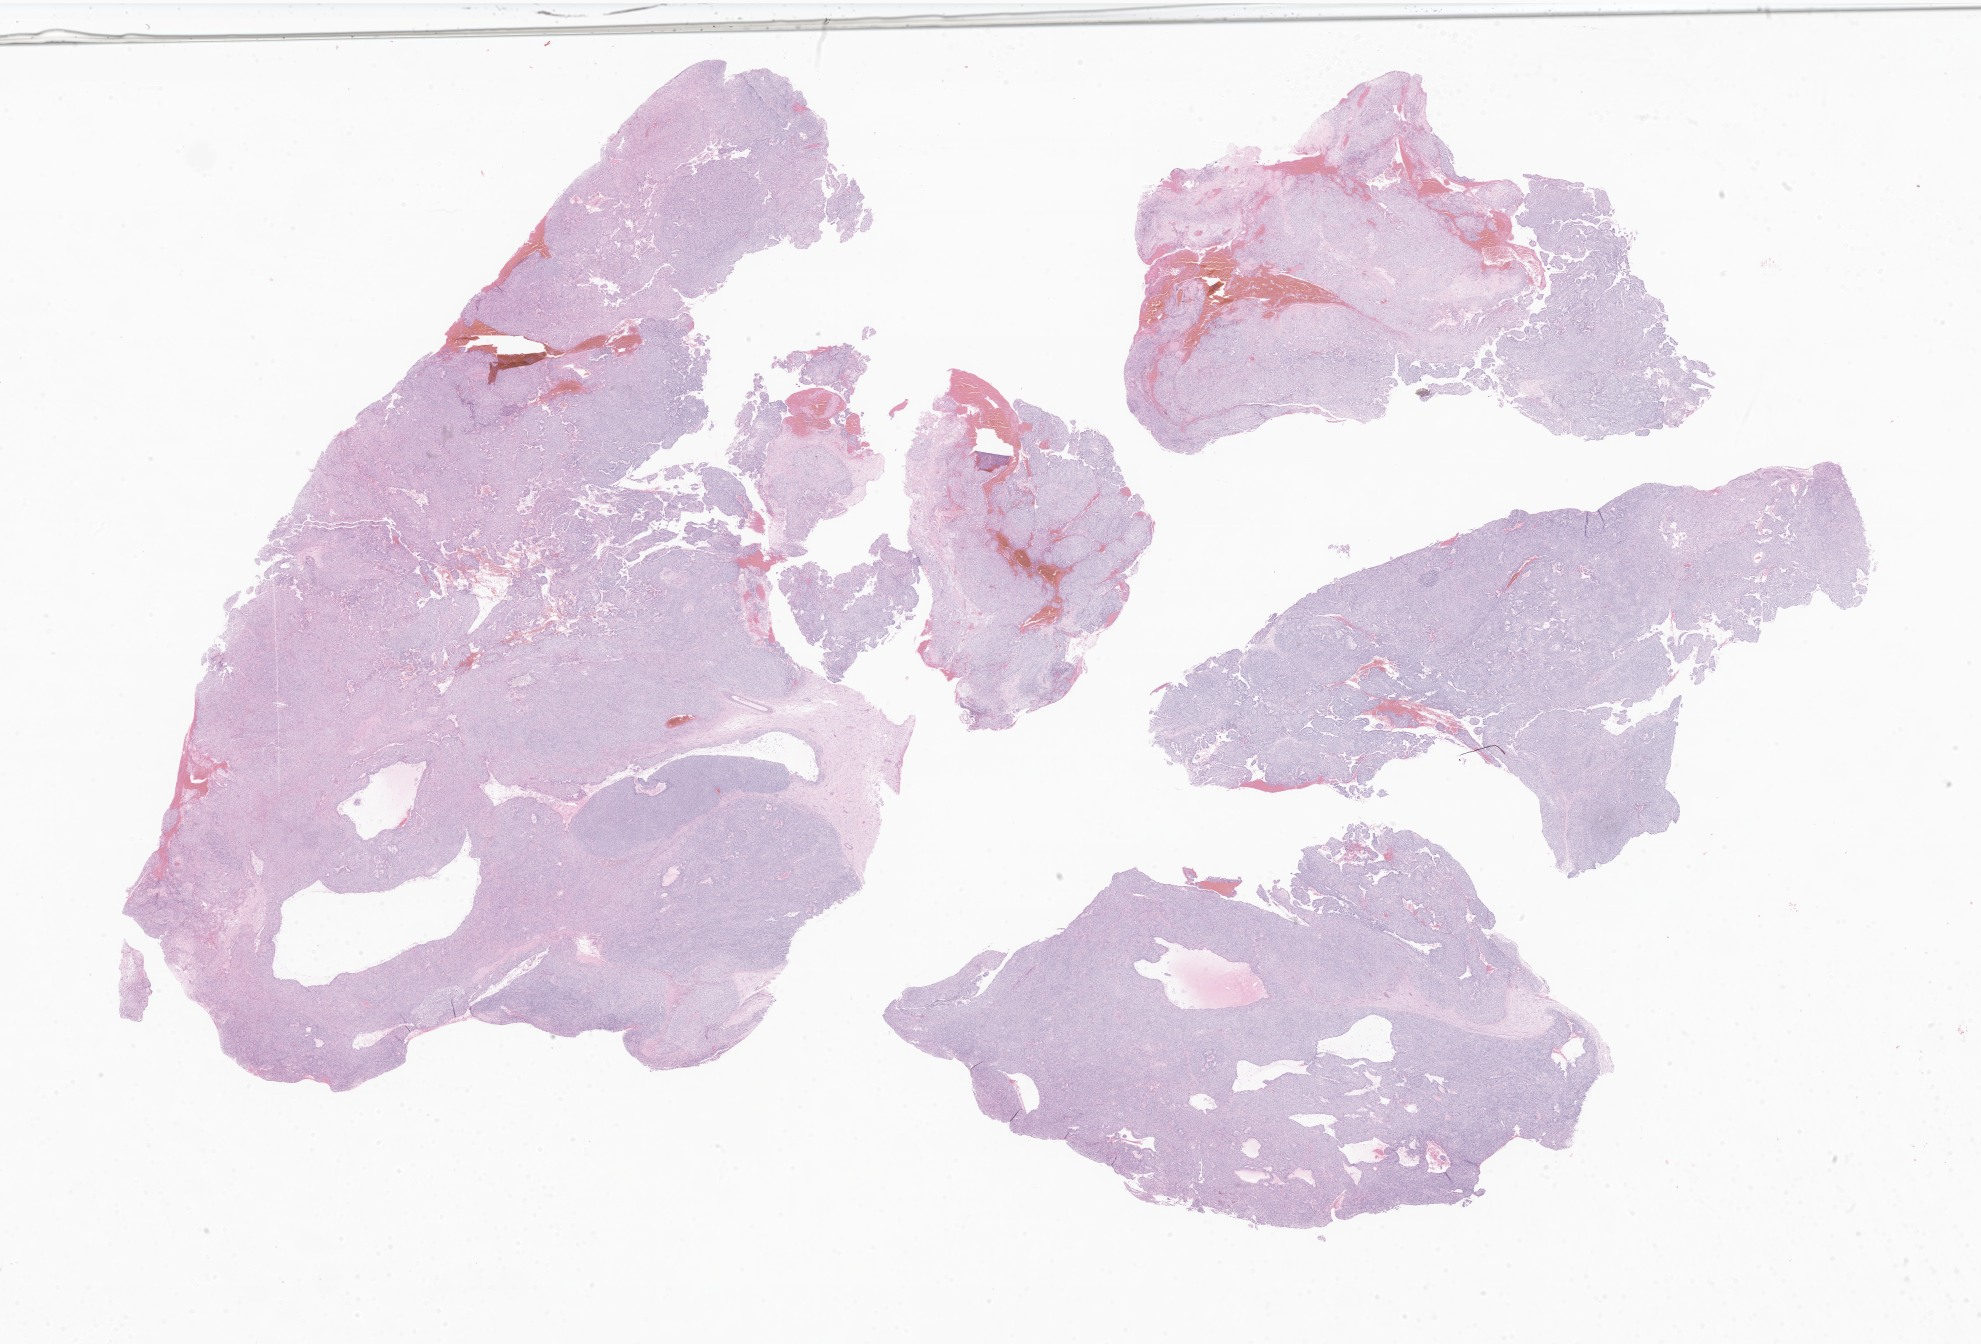
Whole-slide image, hematoxylin and eosin (H&E) stain of tumor tissue from the parietal lobe — a low-resolution overview of the entire scanned area, about 33.4 x 22.7 mm. FFPE section. Patient: female, age 45 months (3 years 9 months).
• diagnosis (ICD-O-3 morphology term): Astroblastoma